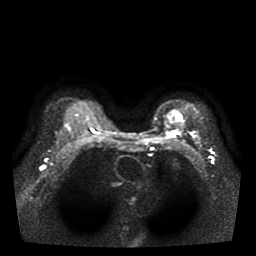
Breast MRI, one axial slice; slice 28 of 39 in the series (ordered by position); diffusion-weighted series; image 2 of 4 stored at this slice position (different b-values; order by instance number); 1.5 T; 5 mm slice thickness; 256 × 256 image matrix, field of view 330 × 330 mm. Female patient.
Outlined on this slice (outlined manually by an expert reader):
- tumour on diffusion-weighted imaging: box from (x=173, y=131) to (x=180, y=134) px